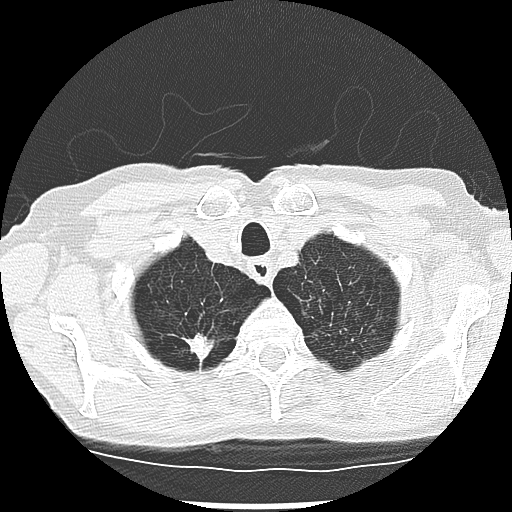
Low-dose screening chest CT, one axial slice; slice 241 of 265 in the series (ordered by position); 120 kVp; lung window (W 1500 / L -600 HU); 2.5 mm slice thickness; 512 × 512 image matrix.
Outlined on this slice (manually delineated by an expert):
- lesion 2 (tumor, upper lobe of right lung): bounding box (x1, y1, x2, y2) in pixels: (186, 334, 213, 360)